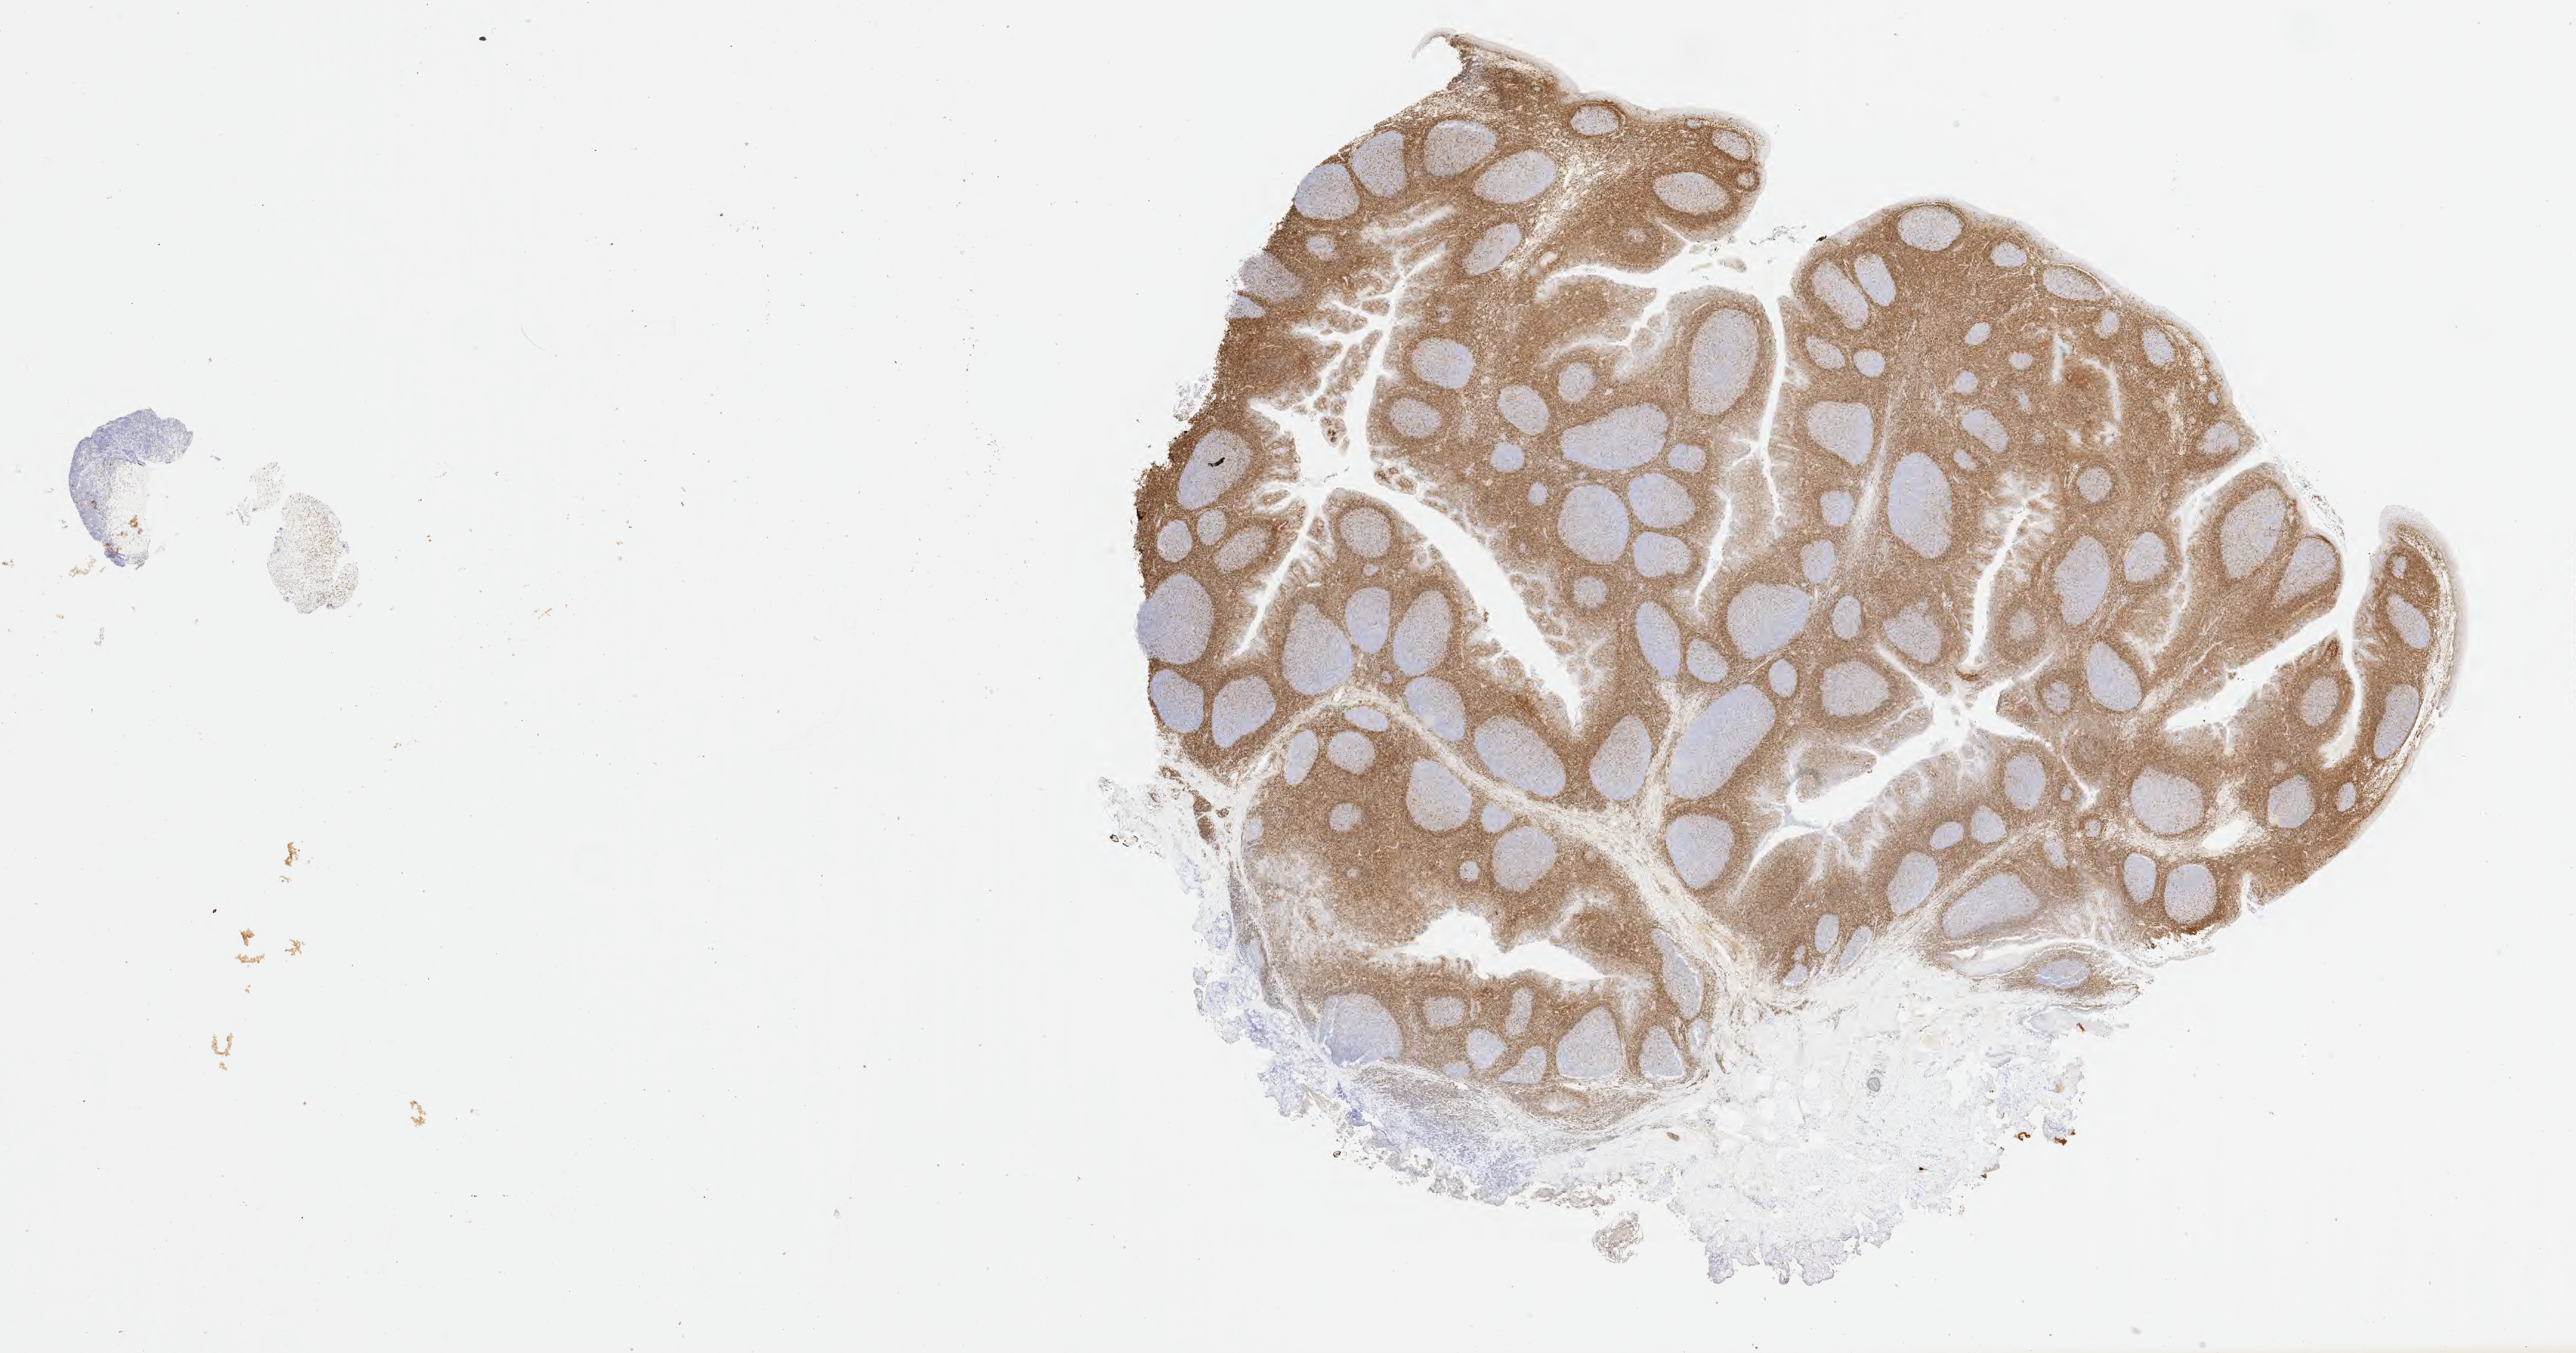
Immunohistochemistry (IHC) whole-slide image stained for BCL2, a low-resolution overview of the entire scanned area, about 28.2 x 14.8 mm. Tumor tissue. Site: abdomen proper. Patient: female, age at initial diagnosis 6 years.
Histologic diagnosis: Diffuse large B-cell lymphoma, NOS.